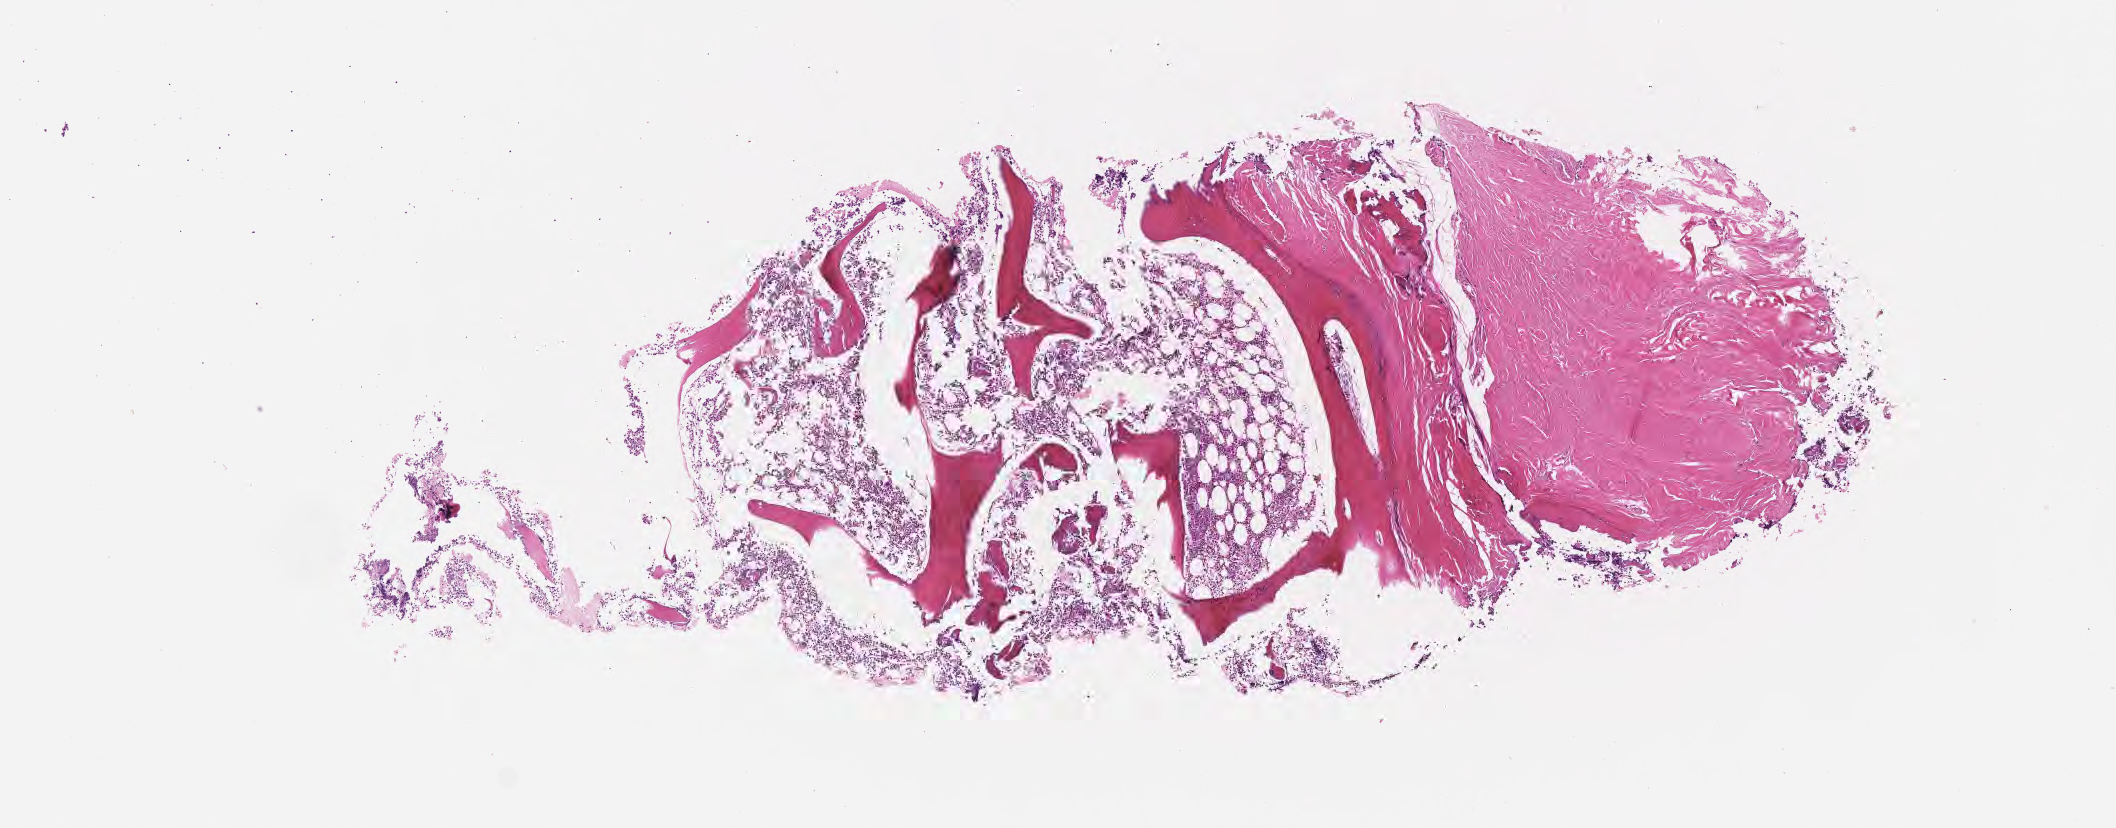
Digitized hematoxylin and eosin (H&E)-stained section — a low-resolution overview of the entire scanned area, about 8.6 x 3.3 mm; formalin-fixed, paraffin-embedded (FFPE) tissue; normal-tissue sample (non-tumor) from a patient with burkitt lymphoma, NOS. Patient male; aged 31.
This section: non-tumor tissue sample; the patient's diagnosis is given above. Section: bottom of the tissue portion.